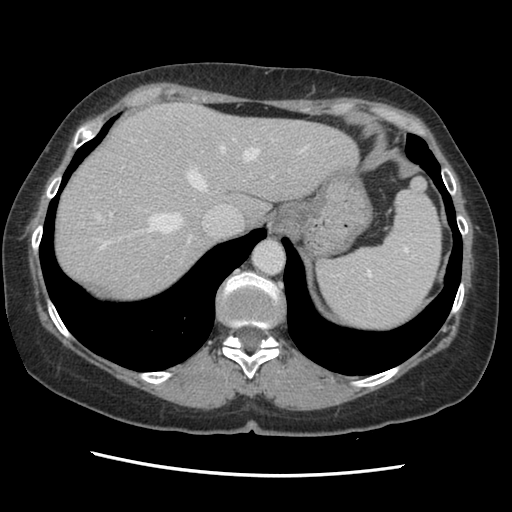
Contrast-enhanced abdominal CT, one axial slice. Slice 109 of 141 in the series (ordered by position). 120 kVp. Soft-tissue window (W 400 / L 40 HU). 512 × 512 image matrix, field of view 330 × 330 mm. Female patient, age 61 years. Case-level facts recorded for this patient, not image findings: diagnosis: colorectal cancer liver metastases, imaged before liver resection; multiple liver metastases: no; largest metastasis: 2.4 cm; disease in both lobes: no.
Structures marked on this image (manually delineated by an expert):
- hepatic veins: bounding box (x1, y1, x2, y2) in pixels: (95, 138, 307, 249)
- liver: (55, 104, 356, 304)
- planned liver remnant (the part of the liver to remain after resection): (55, 104, 357, 303)
- portal vein (with intrahepatic branches): (109, 191, 168, 258)